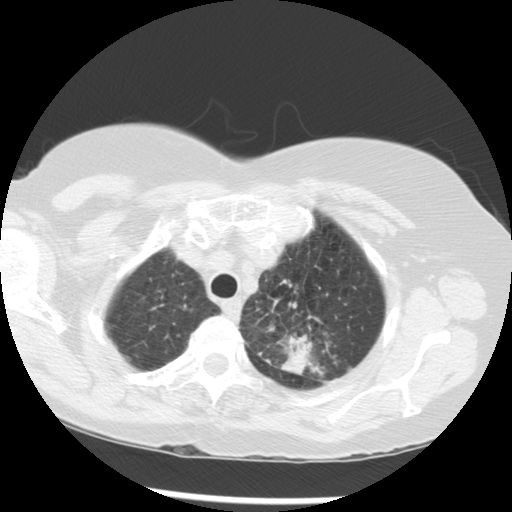
Low-dose screening chest CT, one axial slice; slice 240 of 283 in the series (ordered by position); reconstruction kernel STANDARD; 120 kVp; lung window (W 1500 / L -600 HU); 512 × 512 image matrix, field of view 330 × 330 mm.
Outlined on this slice (outlined manually by an expert reader):
- lesion 1 (tumor, upper lobe of left lung): bounding box [x1, y1, x2, y2] px = [281, 334, 314, 375]